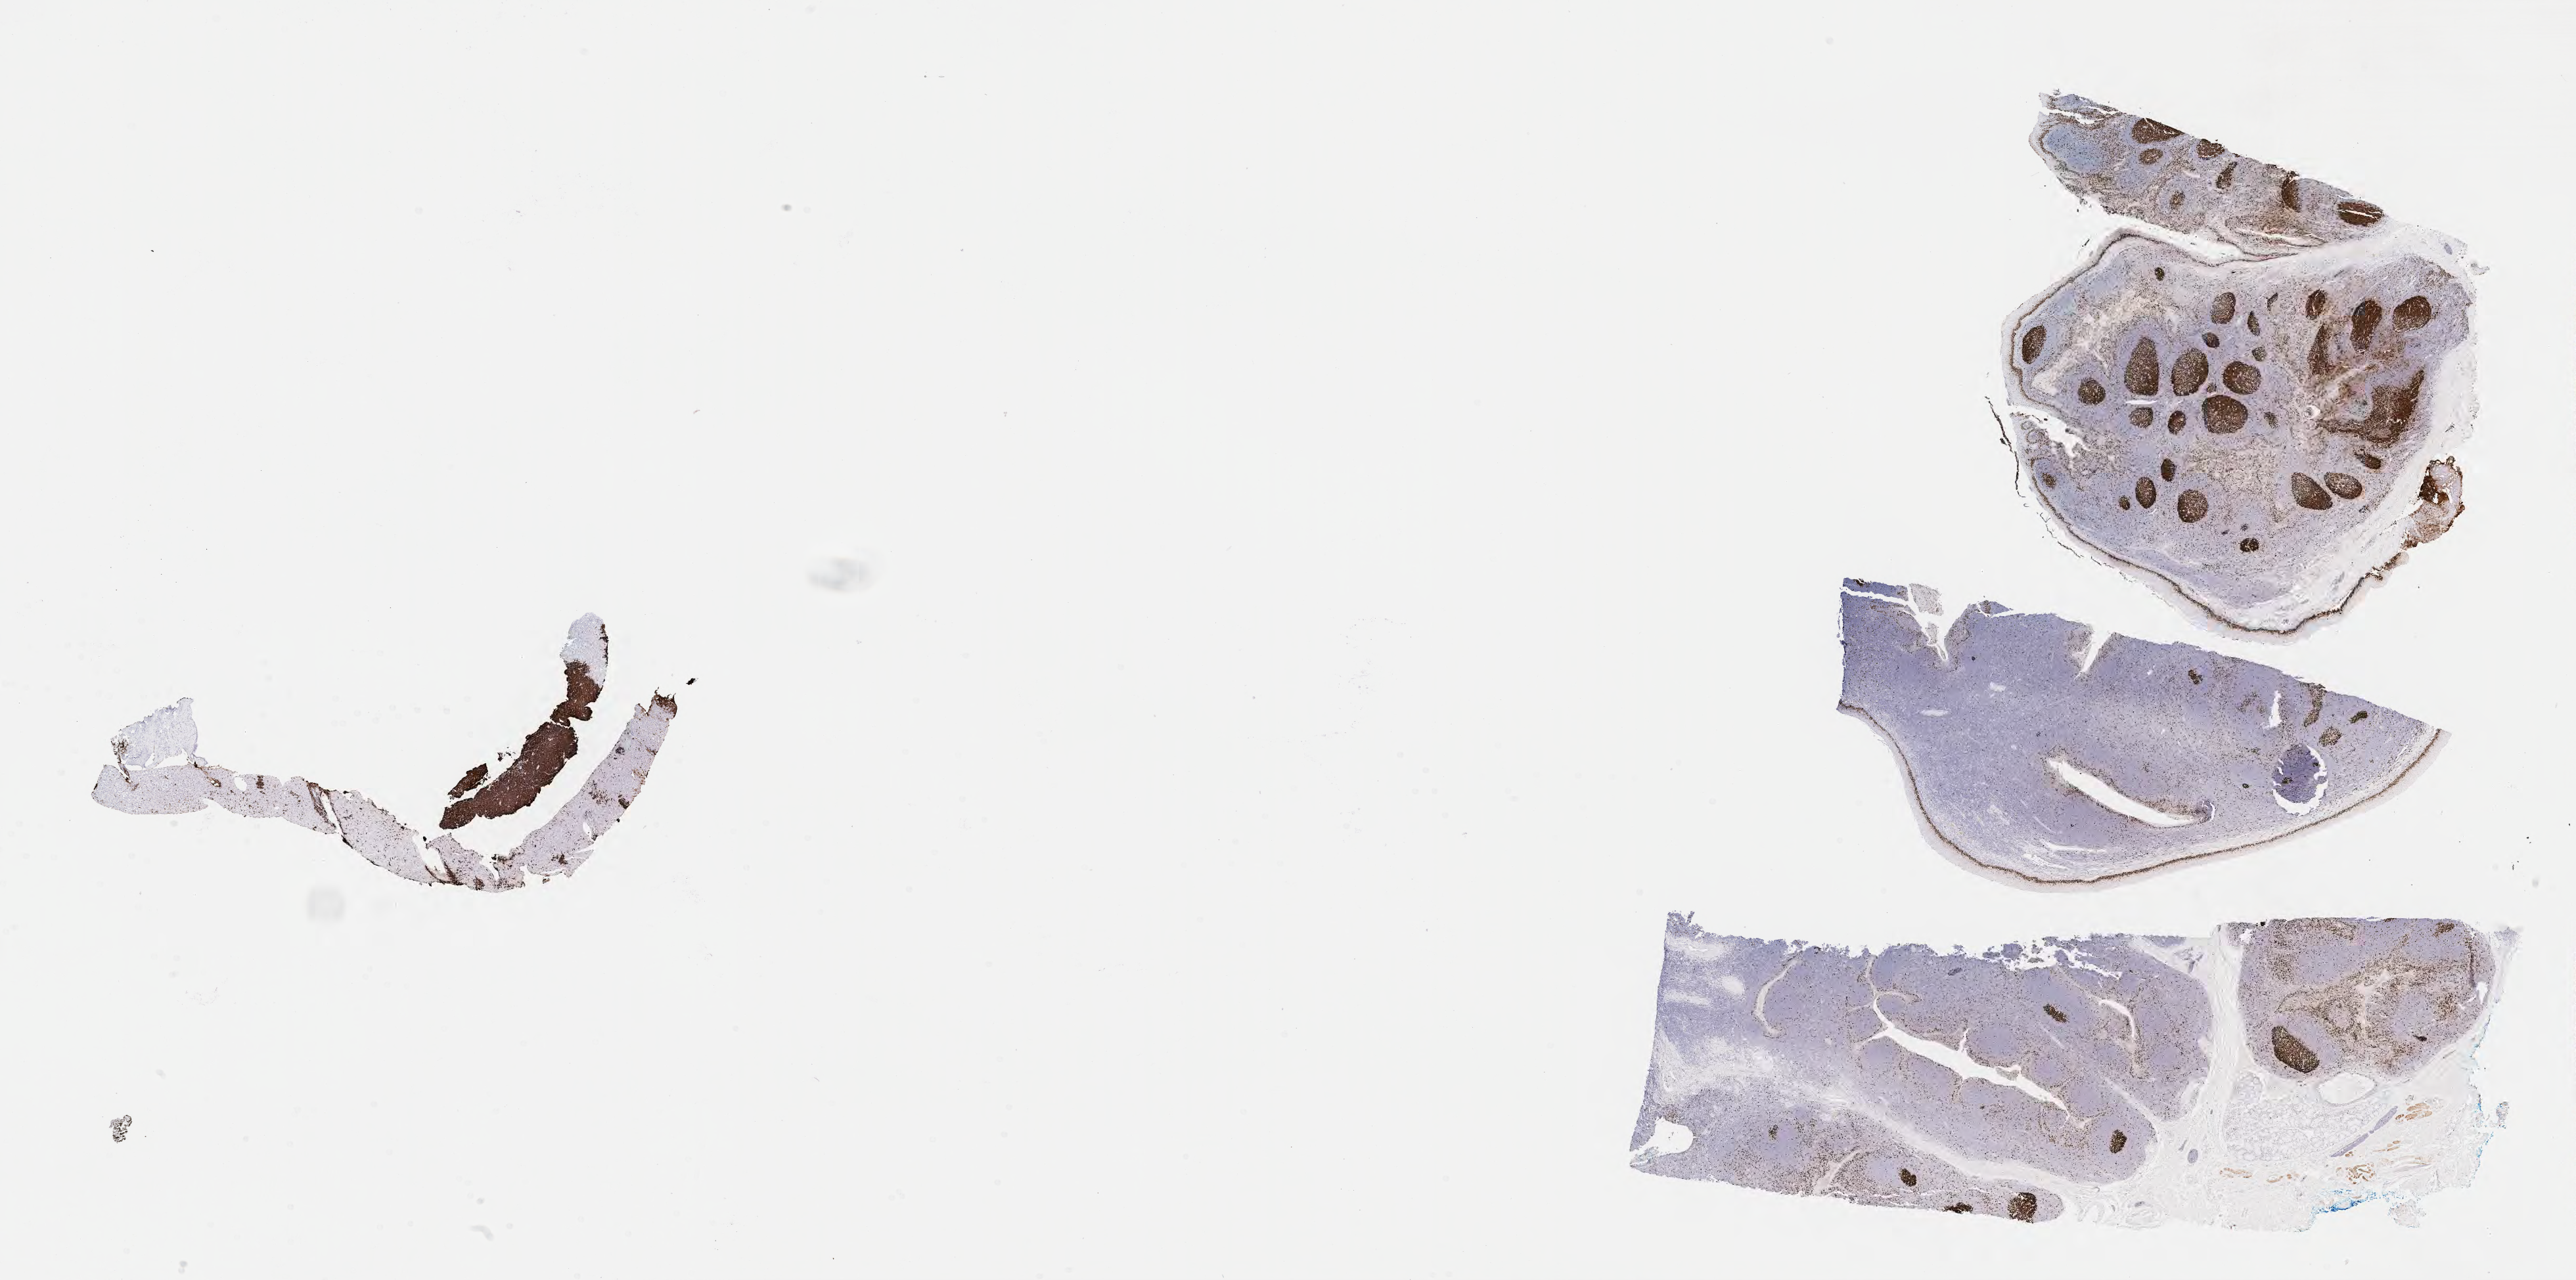
Whole-slide image, immunohistochemical stain for Ki-67 — a low-resolution overview of the entire scanned area, about 31.7 x 15.8 mm. Tumor tissue. Anatomic site: liver. Patient: male, age at initial diagnosis 7 years.
• diagnosis: Burkitt lymphoma, NOS